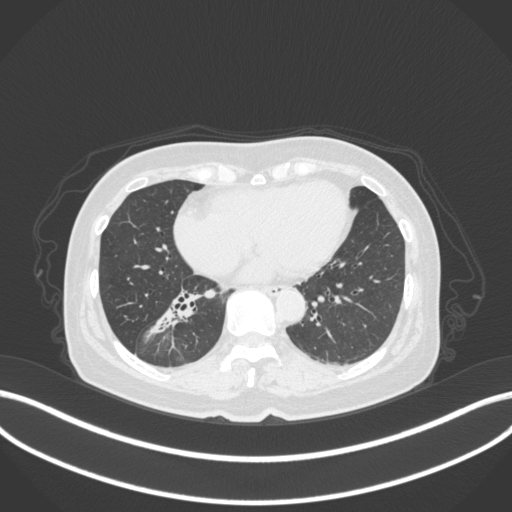
Chest CT, one axial slice; slice 149 of 429 in the series (ordered by position); 120 kVp; lung window (W 1500 / L -600 HU); 1 mm slice thickness; 512 × 512 image matrix, field of view 400 × 400 mm. Patient: female, 67 years. Case-level facts recorded for this patient, not image findings: clinical TNM (as recorded): T1c N1 M0; histopathological grade: G2-3.
Annotated regions visible in this slice (bounding box drawn by a radiologist):
- lung tumour (recorded histology: adenocarcinoma): bounding box [x1, y1, x2, y2] px = [153, 294, 205, 338]